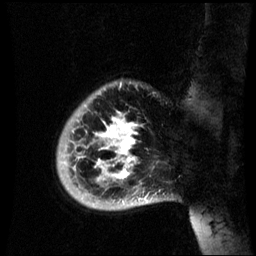
Breast MRI (dynamic contrast-enhanced), one sagittal slice. Slice 9 of 60 in the series (ordered by position). Dynamic contrast-enhanced series, image 2 of 3 at this slice position (ordered by acquisition). 1.5 T. TE 4.2 ms, TR 8.9 ms. 2.6 mm slice thickness. 256 × 256 image matrix, field of view 220 × 220 mm. Female patient, age 35 years. Case-level facts recorded for this patient, not image findings: setting: breast cancer imaged before/during neoadjuvant chemotherapy; receptor status: HR-positive, HER2-negative.
Annotated regions visible in this slice (semi-automatically segmented with operator editing):
- analysis volume of interest (the breast-tissue region the enhancement analysis was run in; not a lesion): box from (x=56, y=80) to (x=164, y=211) px
- tumour enhancement mask (voxels above the 70 % enhancement threshold inside the analysis volume of interest): (x=96, y=112)–(x=137, y=181)